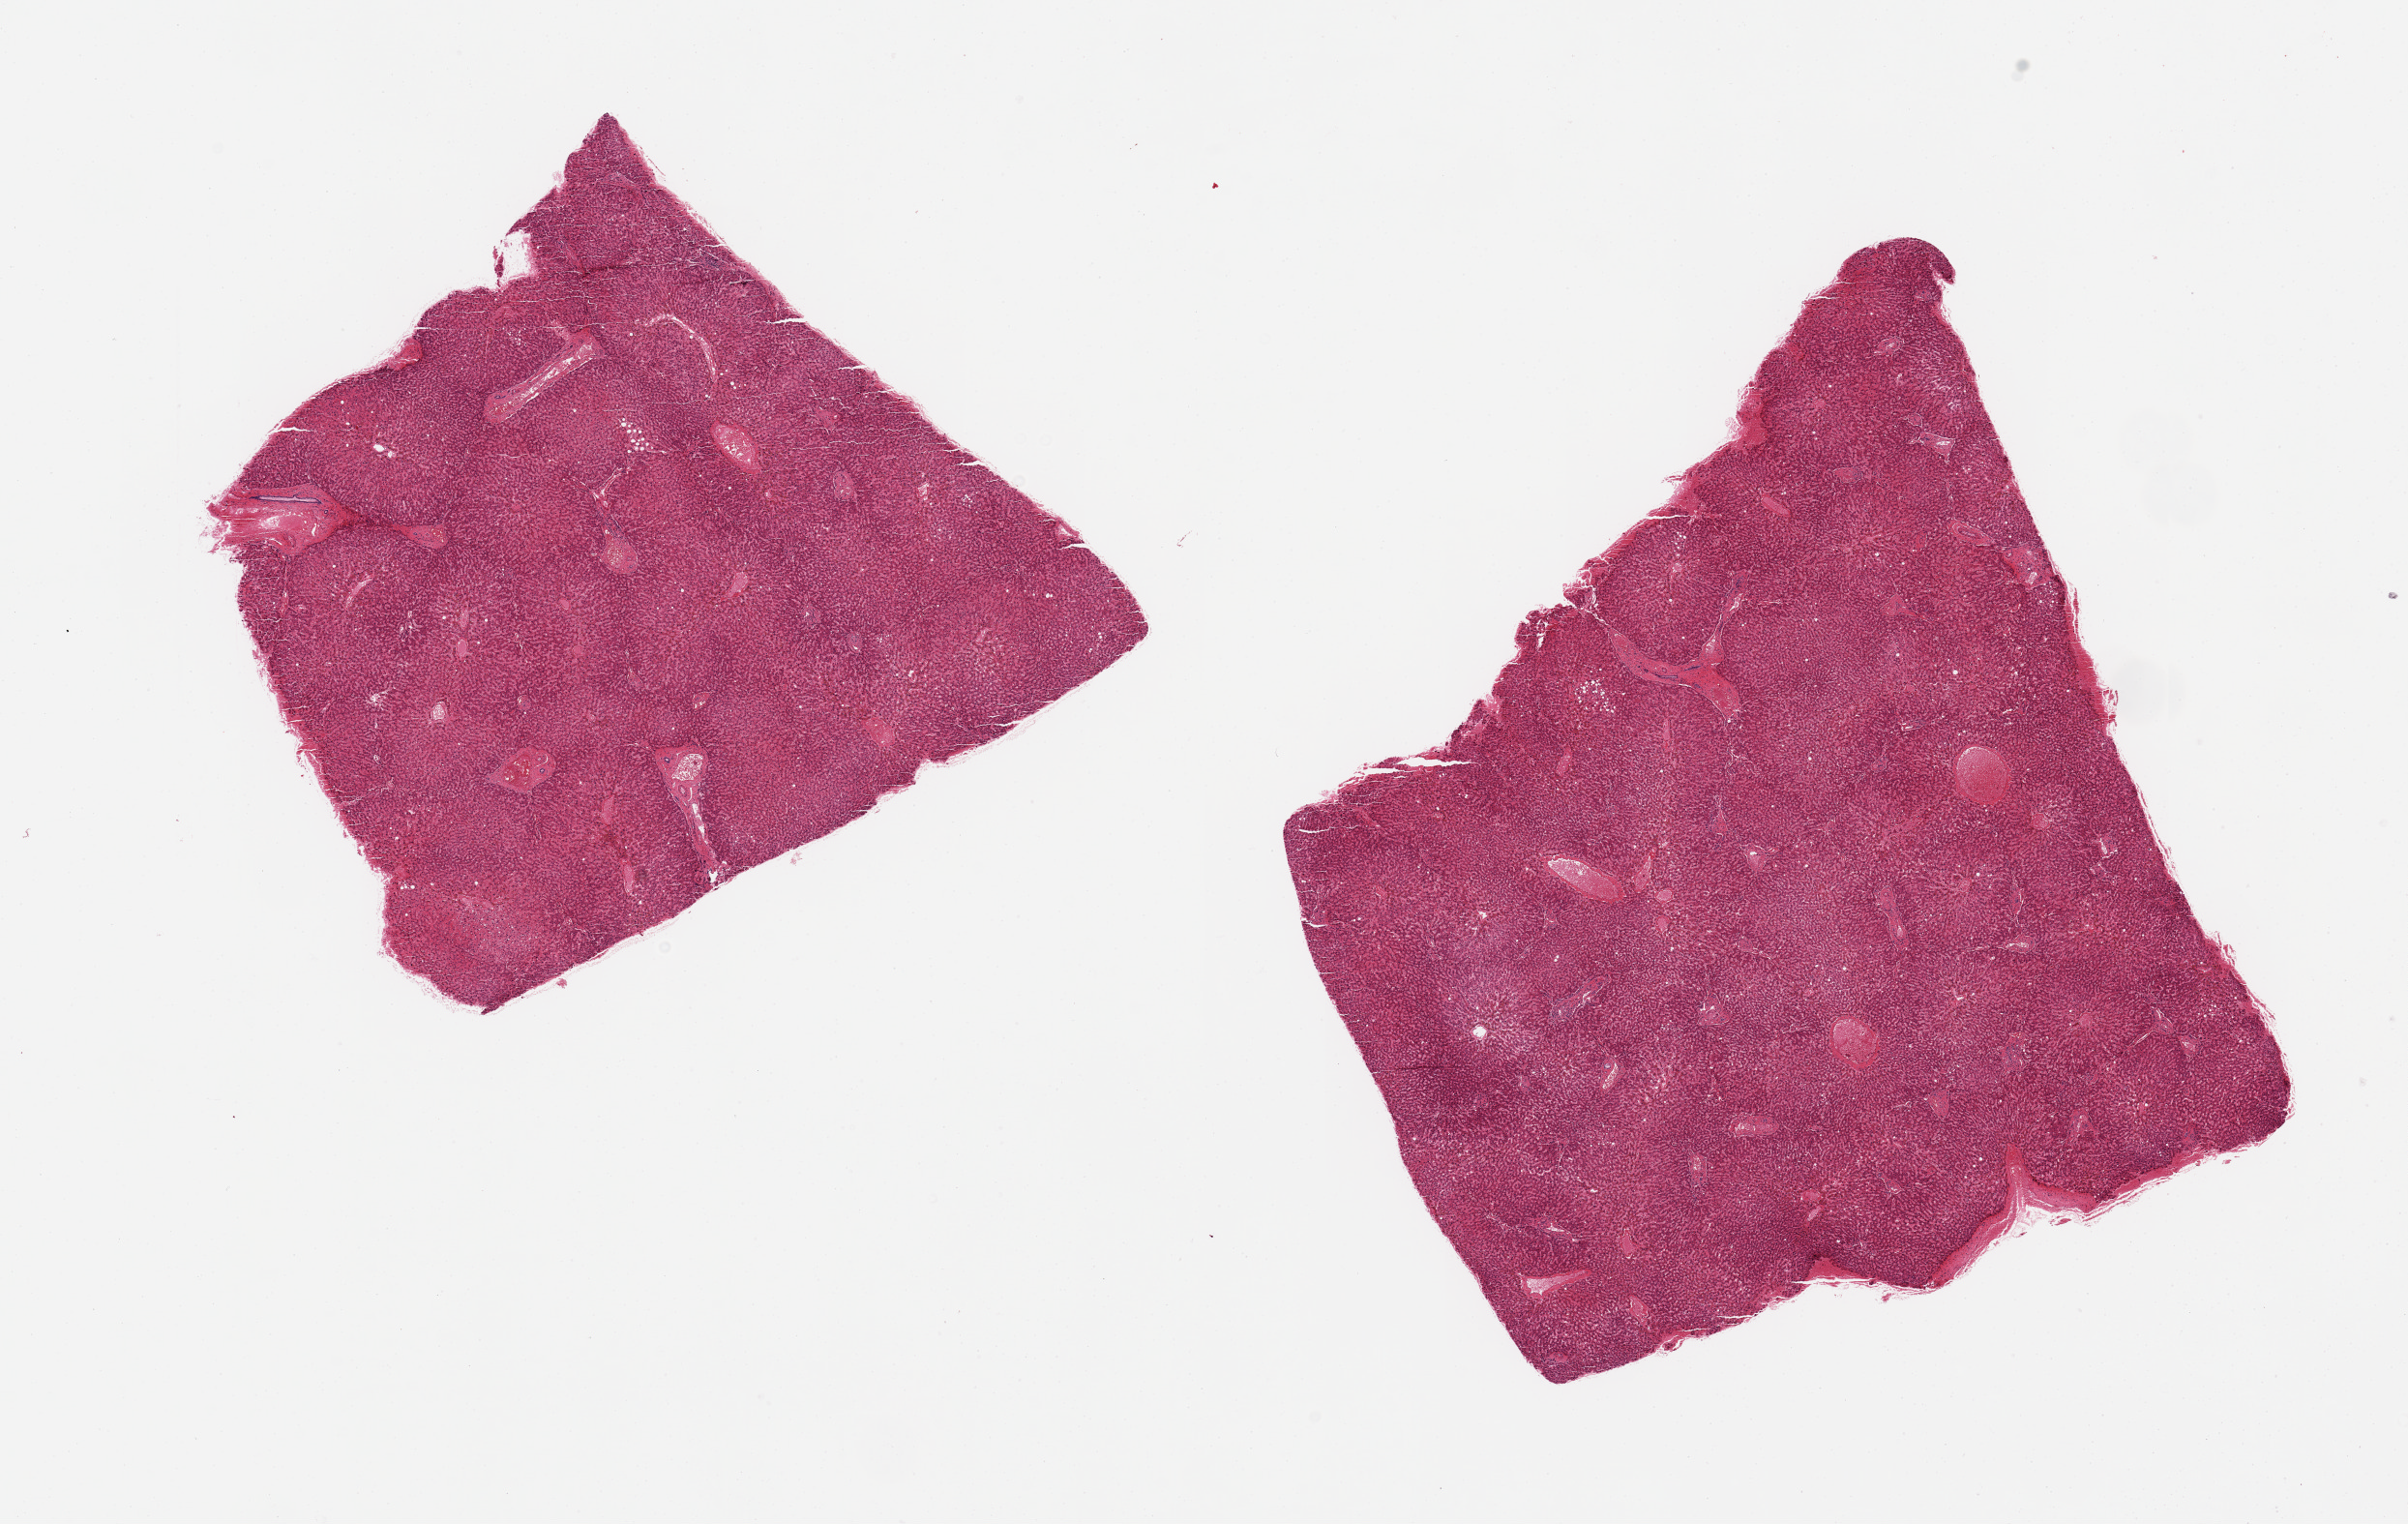
Whole-slide image, H&E stain, a low-resolution overview of the entire scanned area, about 19.7 x 12.5 mm (slide scanned at 20x); PAXgene-fixed, paraffin-embedded tissue; section of liver (target tissue); tissue donor sample. Donor sex: female.
Review note (as recorded): 2 pieces; slight congestion.